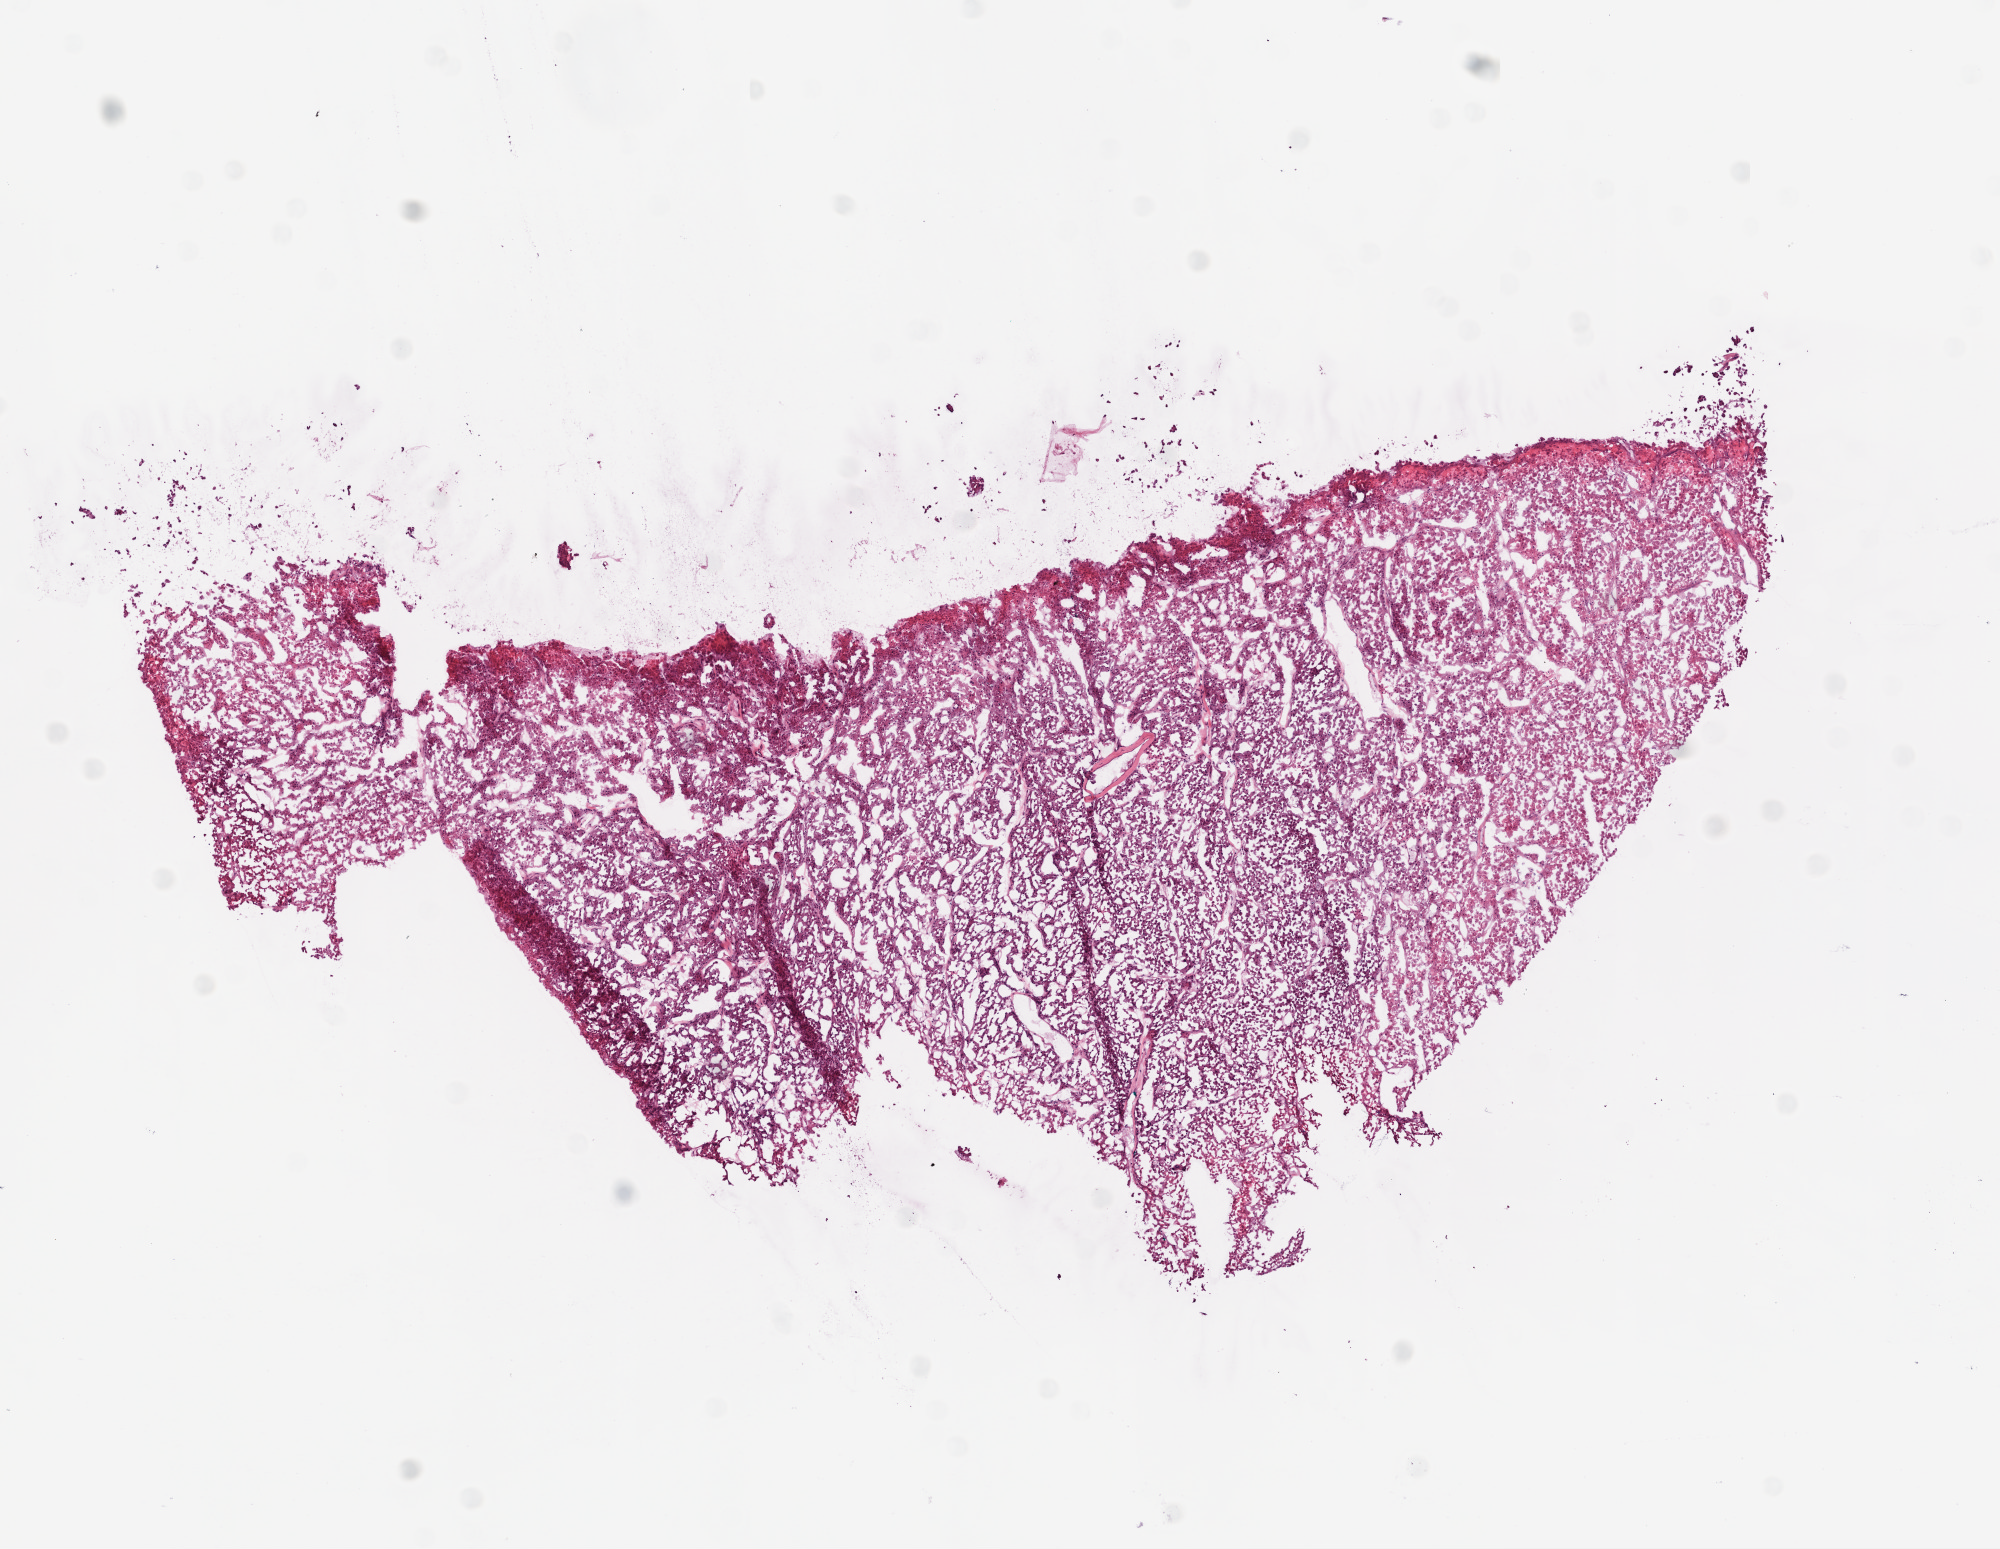
Digitized H&E tissue section (whole slide), whole scanned area (about 8.0 x 6.2 mm) shown as a low-resolution overview. Frozen section. Sample: primary tumour, kidney. Female patient; age at initial diagnosis 48 years. Histologic grade: GX (grade cannot be assessed). Composition of this section per pathologist review: tumour cells 95%, tumour nuclei 85%, normal cells 0%, stromal cells 5%, necrosis 0%.
TNM: T2 N0 M0. Histologic diagnosis: Clear cell adenocarcinoma, NOS. AJCC pathologic stage: II (6th edition).